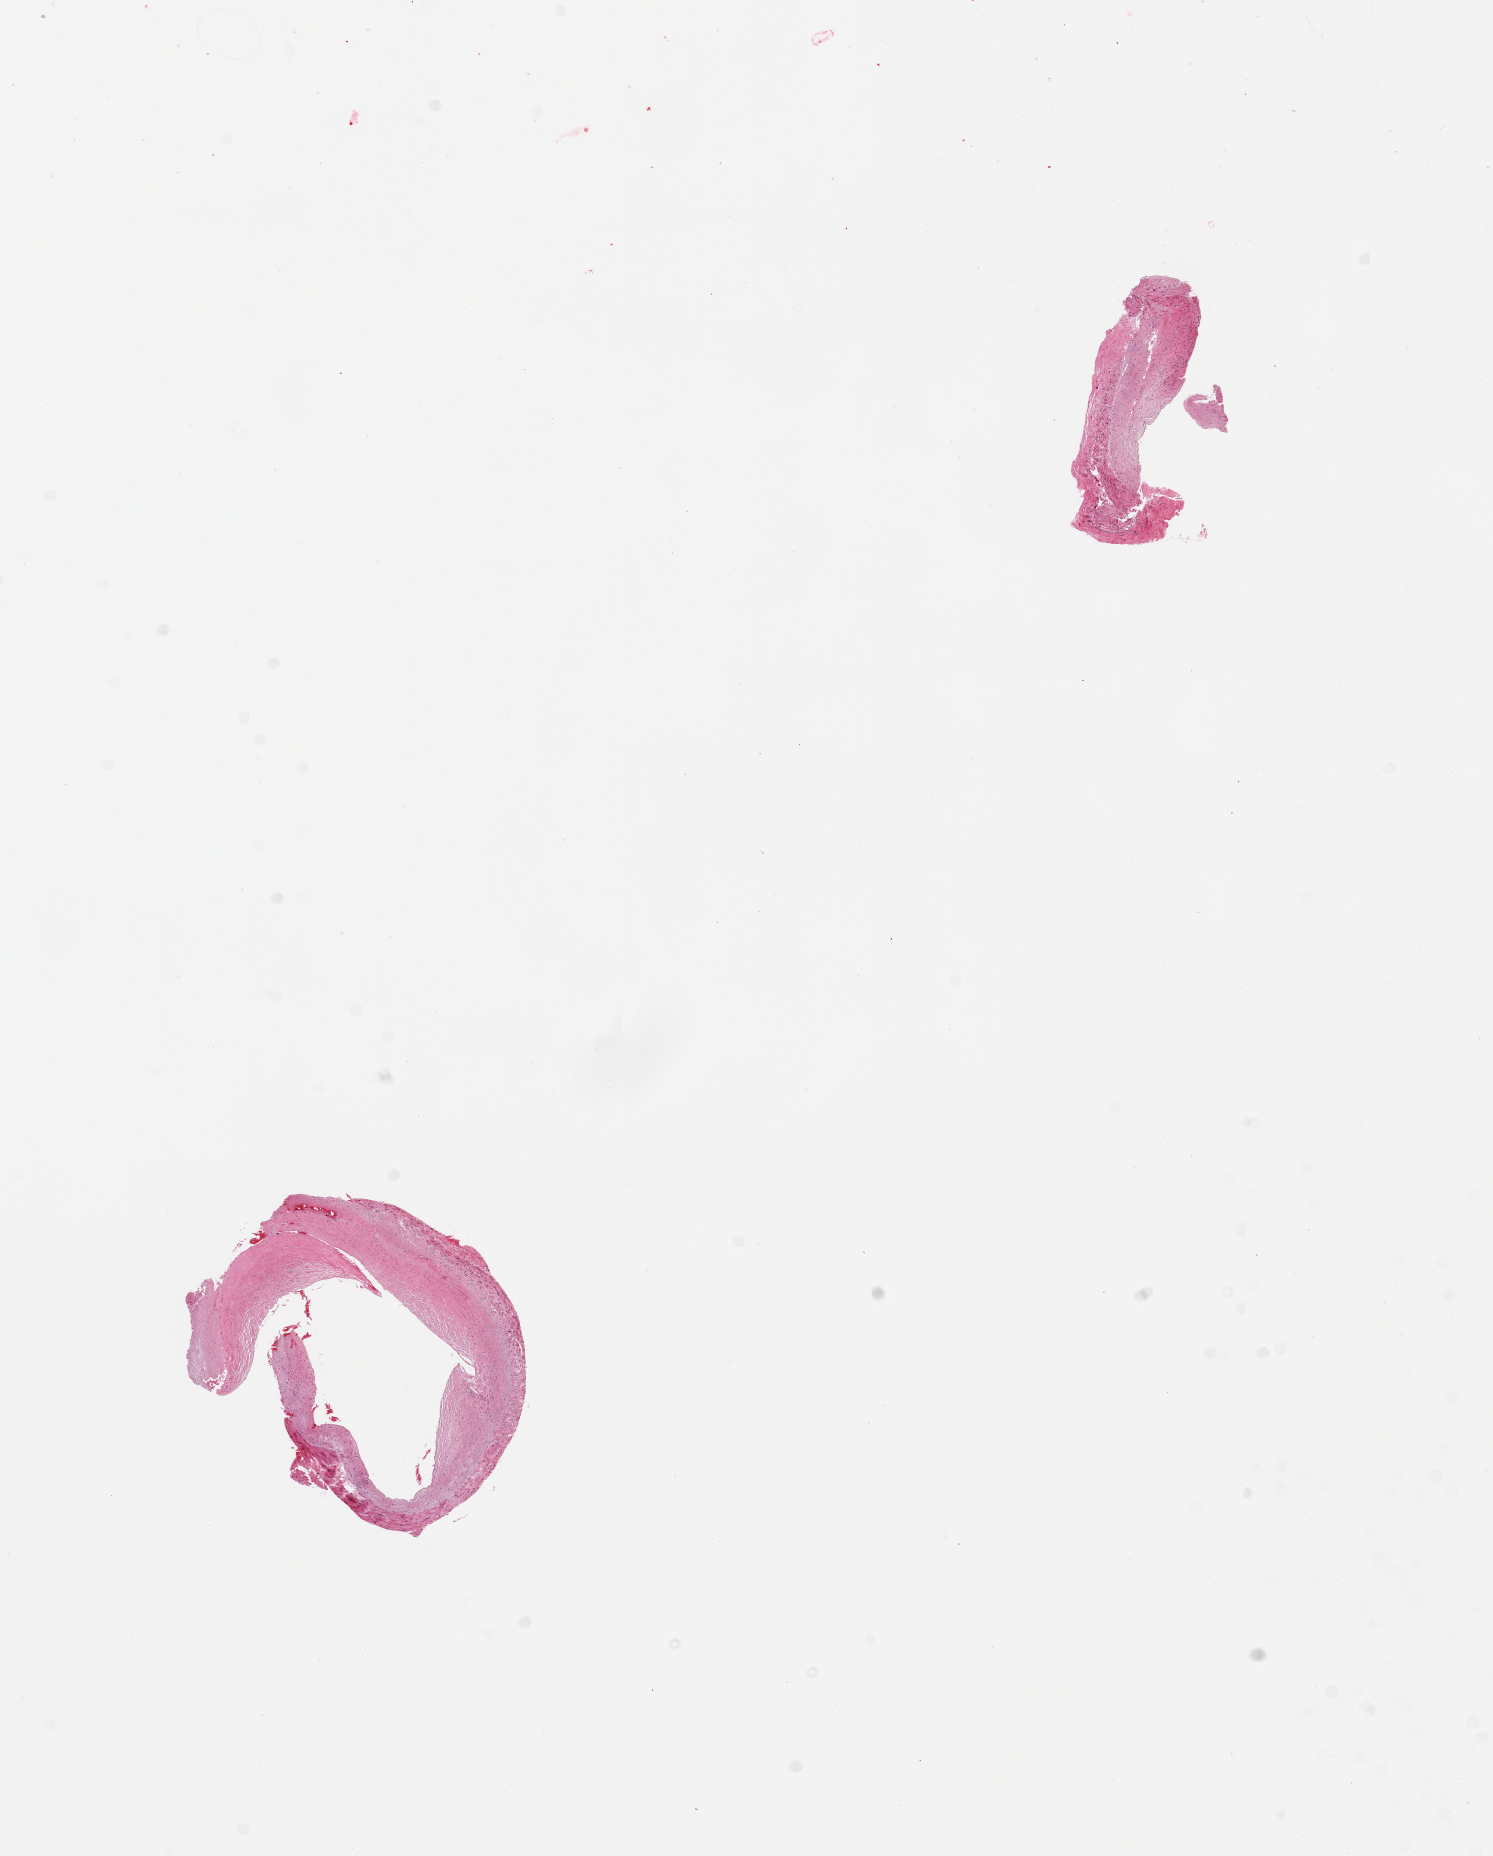
Whole-slide image, H&E stain, brightfield — a low-resolution overview of the entire scanned area, about 11.8 x 14.7 mm, PAXgene-fixed, paraffin-embedded tissue, target tissue: coronary artery, tissue donor sample. Donor sex: female.
* review note (as recorded): 2 pieces, ~30% atherotic occlusion